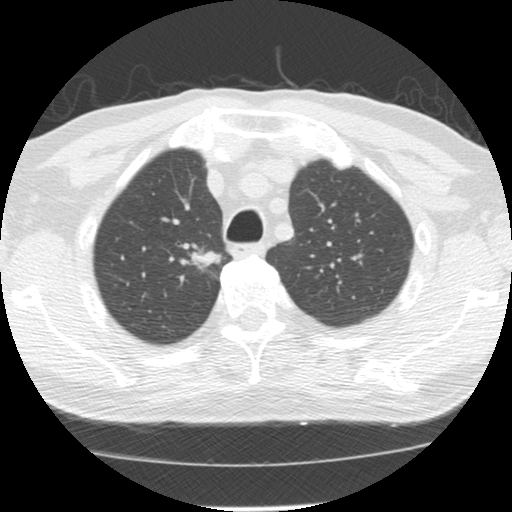
Chest CT (low-dose screening protocol), one axial image. Baseline screening round. Lung window (W 1500 / L -600 HU). Standard (soft-tissue) reconstruction kernel (STANDARD). Slice 33 of 139 in the series. Male, age 64 years at enrolment.
• Expert-annotated lung lesion, bounding box [x1, y1, x2, y2] px = [173, 234, 224, 276].
• The exam's reader record, not a measurement of the box and not confirmed to be the same lesion: non-calcified nodule or mass ≥4 mm, right upper lobe, 20 × 13 mm, spiculated (stellate) margins, soft tissue attenuation.
• Lung cancer was diagnosed 73 days after this screen: adenocarcinoma, NOS, right upper lobe, moderately differentiated (G2), stage IA (AJCC 6th edition), 17 mm at pathology.